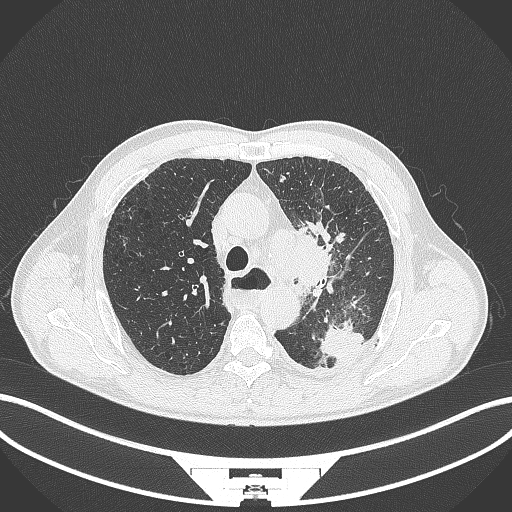
Chest CT, one axial slice. Slice 276 of 411 in the series (ordered by position). Reconstruction kernel B70f. 120 kVp. Lung window (W 1500 / L -600 HU). 1 mm slice thickness. 512 × 512 image matrix. Patient: male, 57 years. Case-level facts recorded for this patient, not image findings: clinical TNM (as recorded): T2a N1 M0.
Structures marked on this image (rectangle marked by the reading radiologist):
- lung tumour (recorded histology: squamous cell carcinoma): box from (x=291, y=229) to (x=334, y=293) px